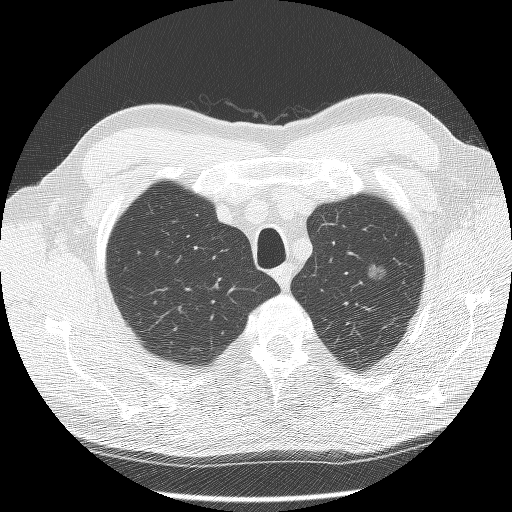
Chest CT (low-dose screening protocol), one axial image. Second screening round (one year after baseline). Lung window (W 1500 / L -600 HU). 2.5 mm slice thickness. Lung (sharp) reconstruction kernel (BONE). 120 kVp. Slice 21 of 124 in the series. 512 × 512 image matrix. Male participant, aged 60 years at enrolment.
• Lesion marked by an expert reader, bounding box (x1, y1, x2, y2) in pixels: (350, 255, 402, 298).
• The screening reader recorded 2 non-calcified nodules or masses ≥4 mm on this exam (right lower lobe, left upper lobe); which of them this box marks is not recorded.
• Participant outcome: lung cancer diagnosed 448 days after this screen — bronchiolo-alveolar carcinoma, non-mucinous, left upper lobe, well differentiated (G1), stage IA (AJCC 6th edition), 16 mm at pathology.